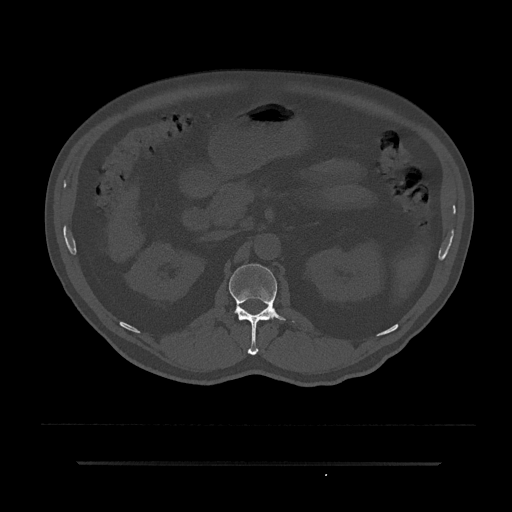
CT including the spine, one axial slice; position 141 of 797 along the scan axis; reconstruction kernel Br40s/3; bone window (W 1800 / L 400 HU); 0.5 mm slice thickness; 512 × 512 image matrix, field of view 464 × 464 mm. Male patient, age 59 years. From the clinical record (not read from this slice): primary cancer: bile ducts.
Outlined on this slice (semi-automatically segmented with operator editing):
- L1 vertebra: bounding box [x1, y1, x2, y2] px = [229, 264, 296, 355]